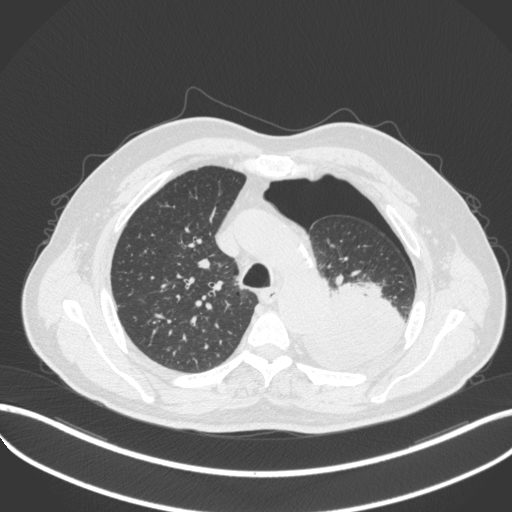
Chest CT, one axial slice. Slice 375 of 466 in the series (ordered by position). 120 kVp. Lung window (W 1500 / L -600 HU). 1 mm slice thickness. 512 × 512 image matrix, field of view 400 × 400 mm. Patient: male, 76 years. Case-level facts recorded for this patient, not image findings: clinical TNM (as recorded): T3 N0 M1b.
Structures marked on this image (rectangle marked by the reading radiologist):
- lung tumour (recorded histology: adenocarcinoma): bounding box (x1, y1, x2, y2) in pixels: (301, 277, 411, 367)